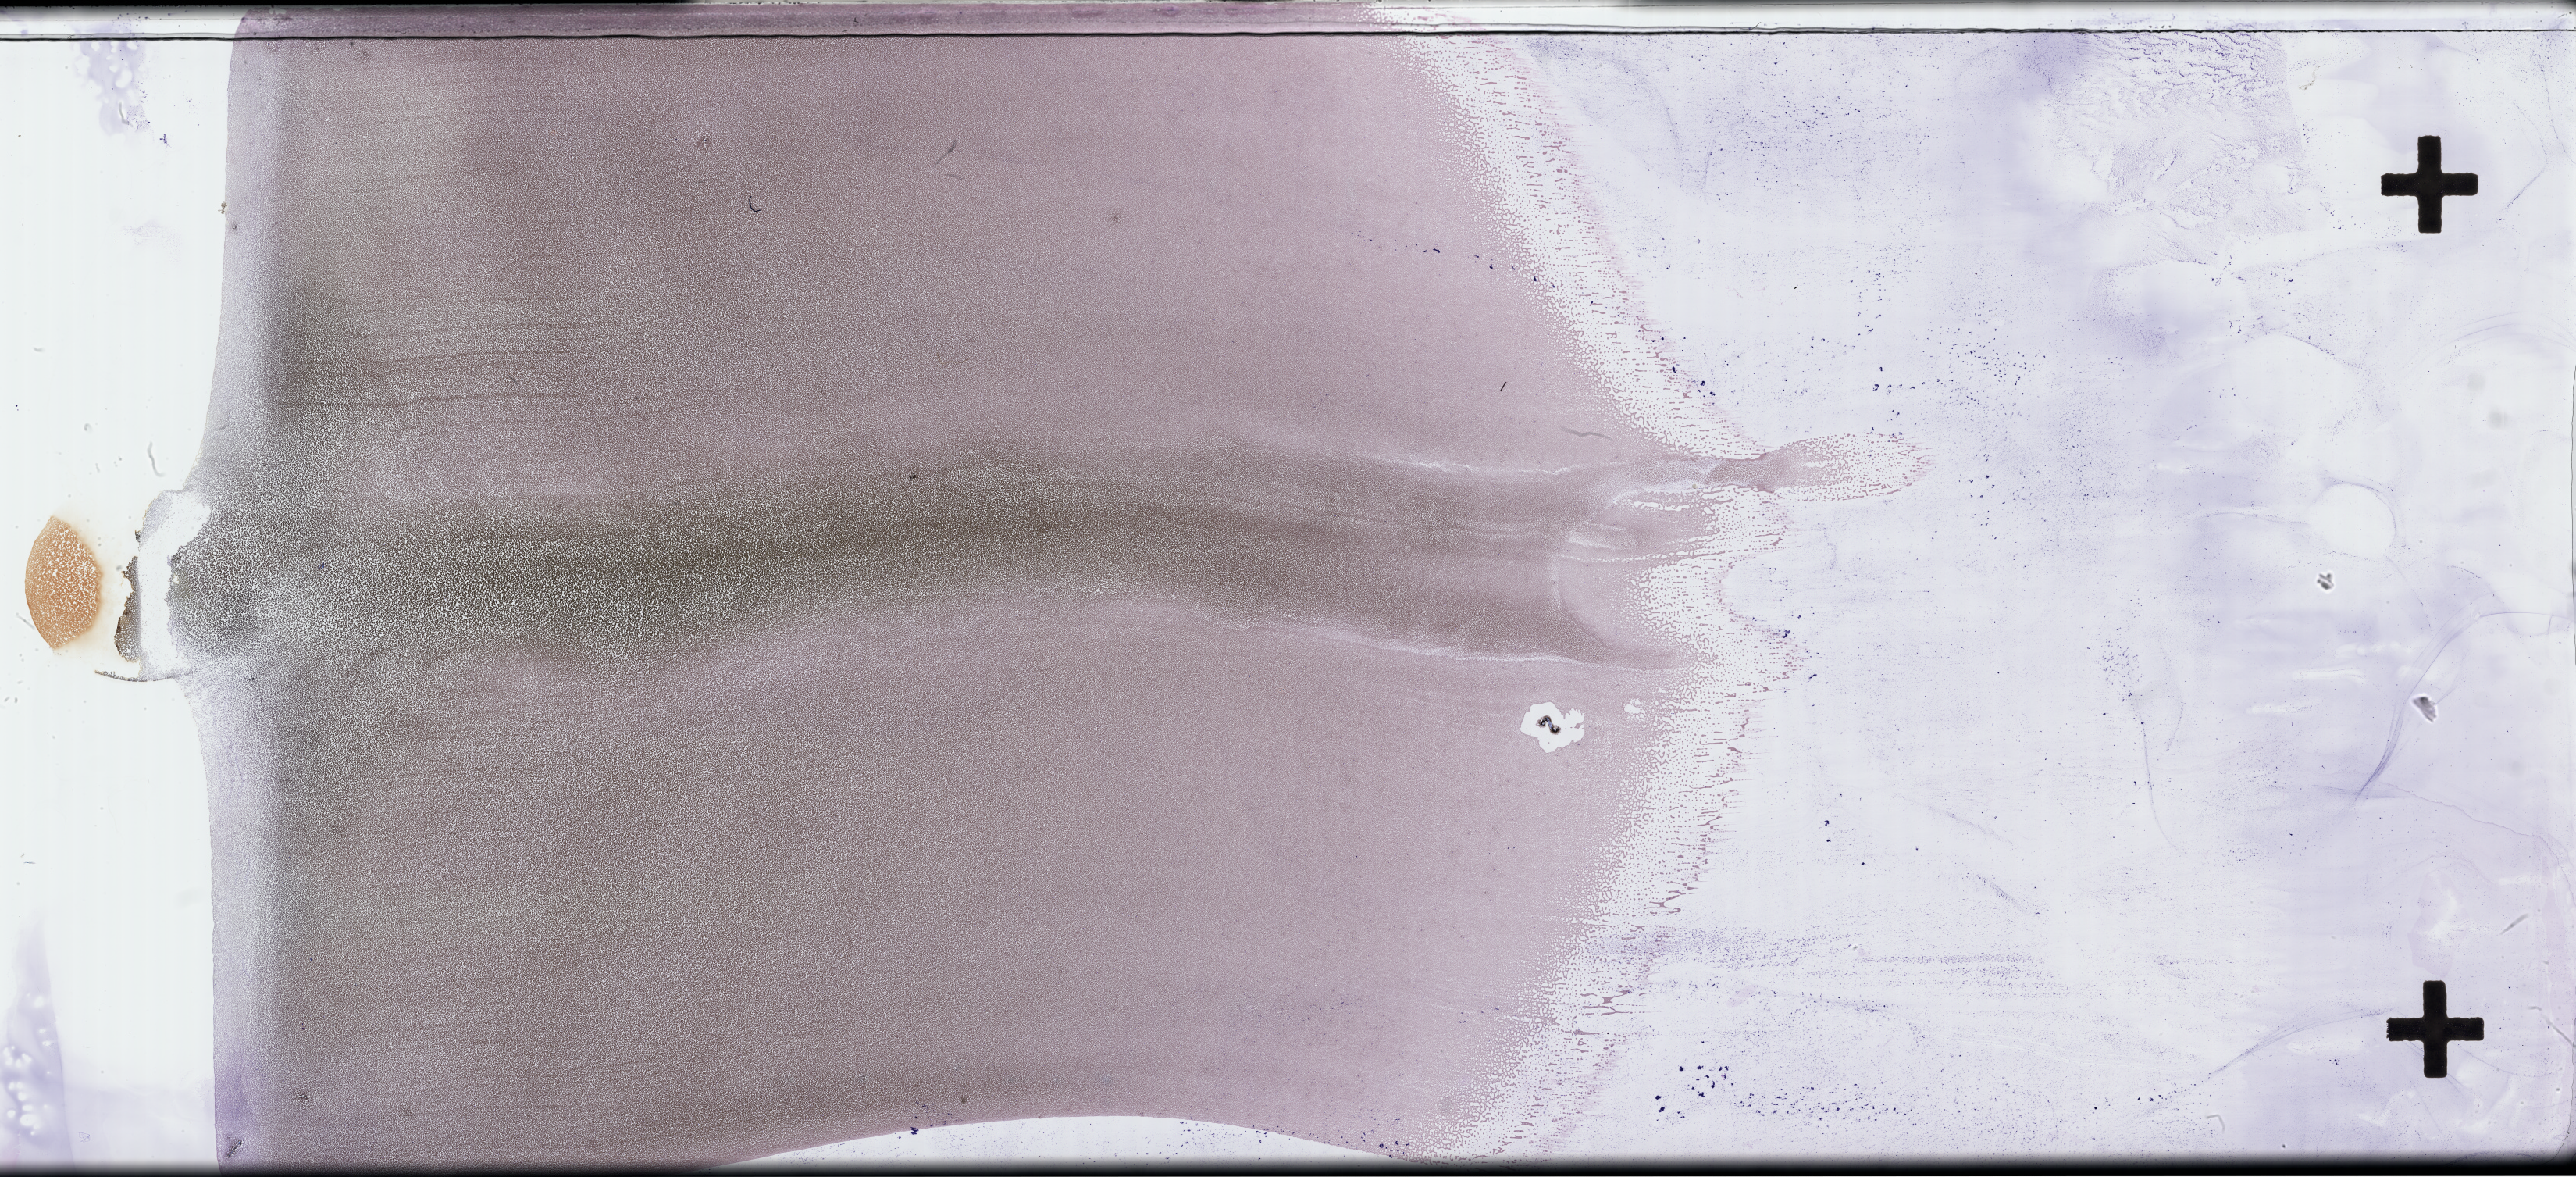
Wright-Giemsa-stained whole blood smear, whole-slide image — shown as a low-resolution overview of the whole scanned area (about 53.3 x 24.3 mm). EDTA-anticoagulated smear. Specimen time point: collected at baseline (before treatment). Male patient.
- from a patient with: Plasma Cell Myeloma